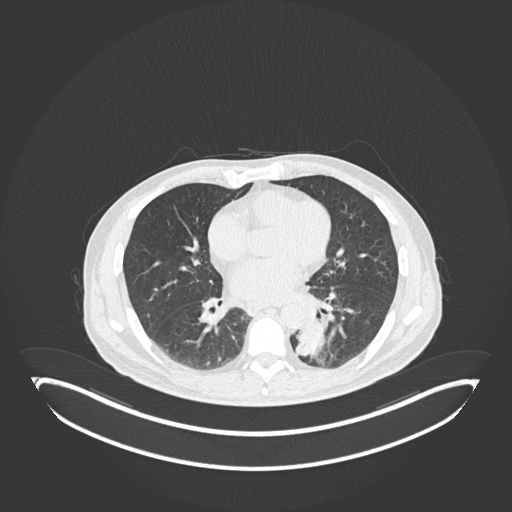
Chest CT, one axial slice; slice 77 of 251 in the series (ordered by position); 120 kVp; lung window (W 1500 / L -600 HU); 512 × 512 image matrix. Patient: male, 72 years. From the clinical record (not read from this slice): clinical TNM (as recorded): T2b N0 M1.
Annotated regions visible in this slice (rectangle marked by the reading radiologist):
- lung tumour (recorded histology: adenocarcinoma): box from (x=294, y=317) to (x=329, y=360) px